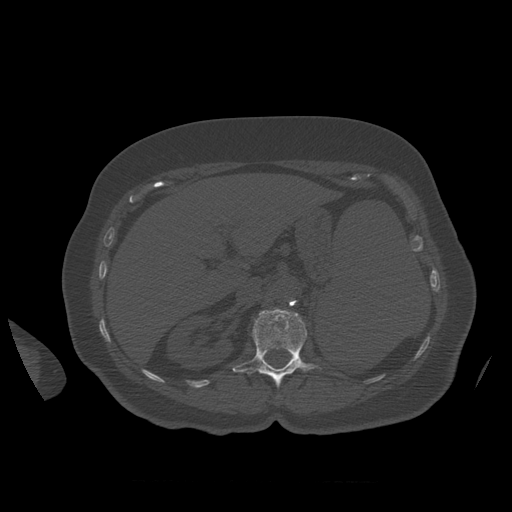
CT including the spine, one axial slice; slice 278 of 399 in the series (ordered by position); bone window (W 1800 / L 400 HU); 1.25 mm slice thickness; 512 × 512 image matrix, field of view 404 × 404 mm. Patient age 81 years. Case-level facts recorded for this patient, not image findings: primary cancer: renal.
Structures marked on this image (semi-automatically segmented with operator editing):
- L1 vertebra: bounding box [x1, y1, x2, y2] px = [233, 308, 322, 388]